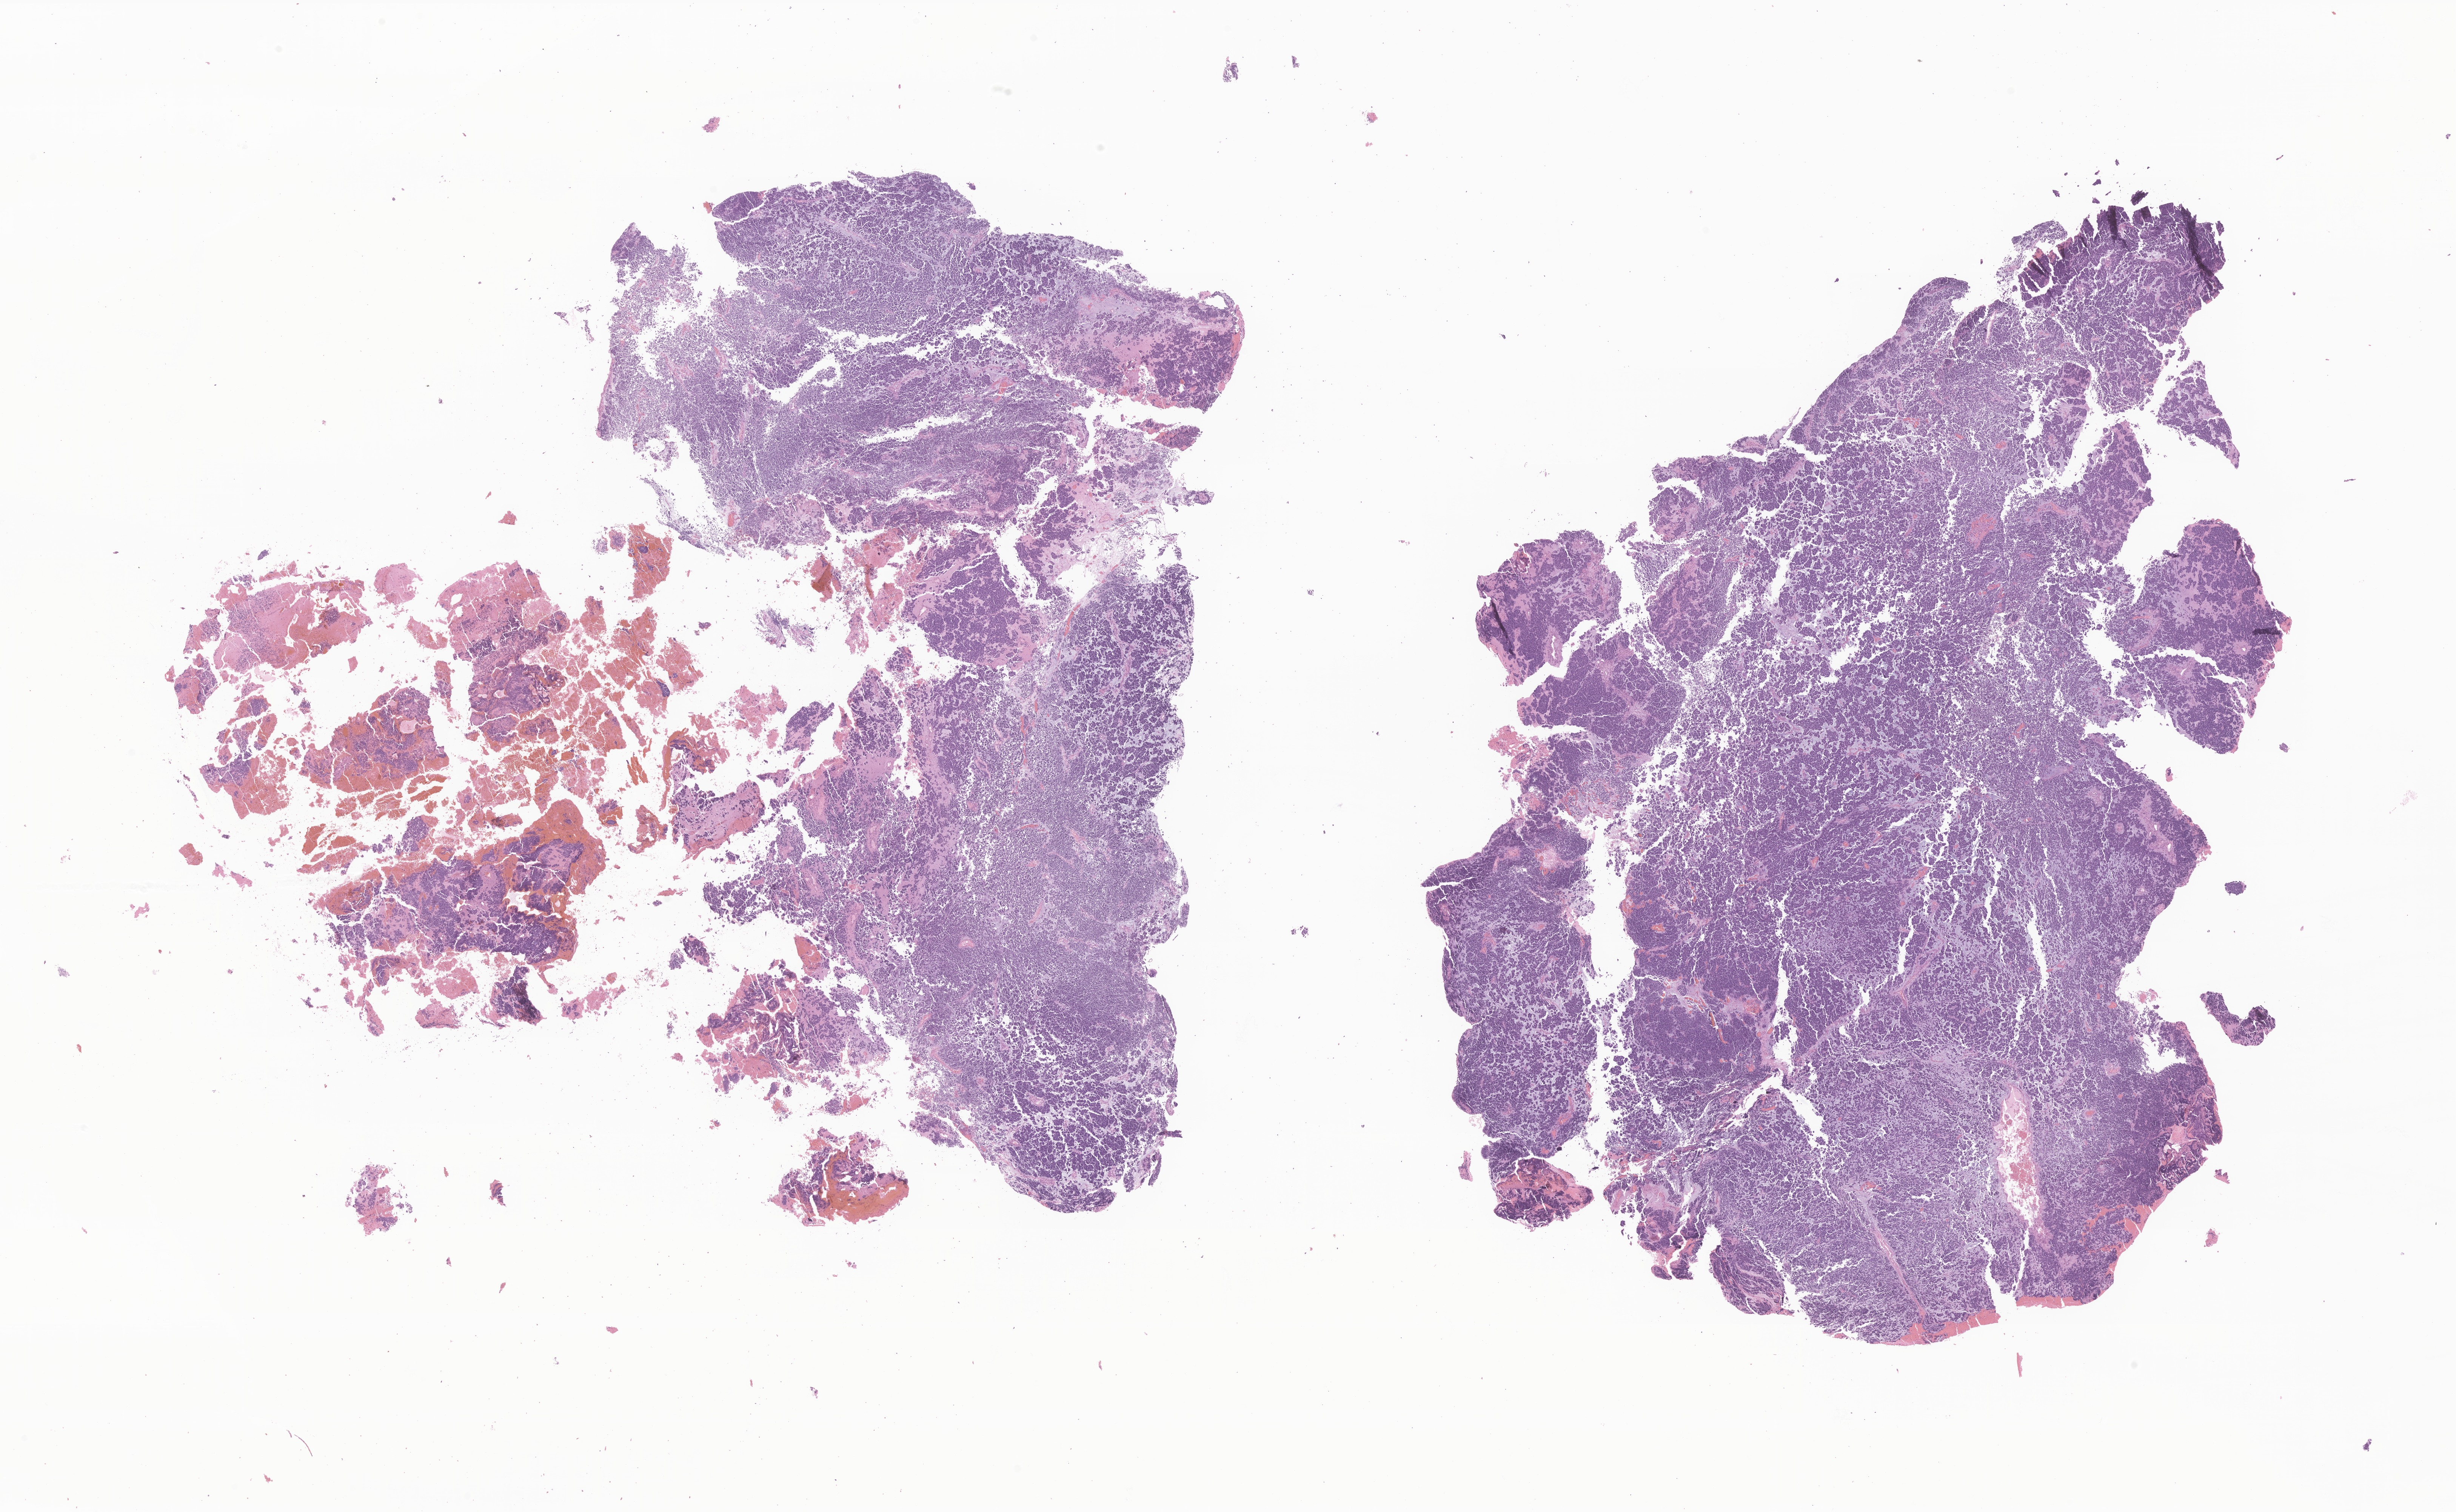
Whole-slide image, haematoxylin and eosin stain of tumor tissue from the central nervous system, a low-resolution overview of the entire scanned area, about 27.4 x 16.9 mm, FFPE section. Male patient, age 74 months (6 years 2 months).
Diagnosis: Medulloblastoma, NOS.